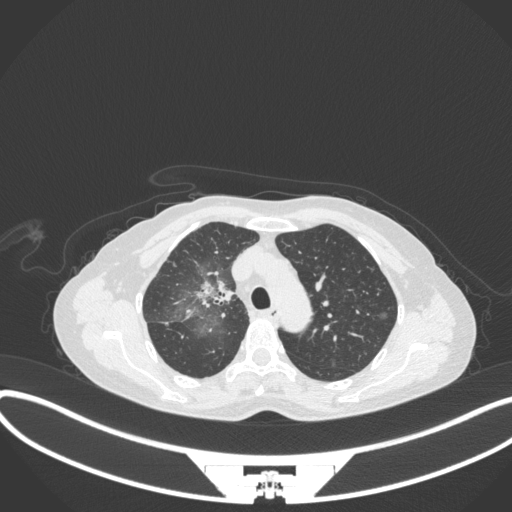
Chest CT, one axial slice. Slice 230 of 311 in the series (ordered by position). Reconstruction kernel B31f. 120 kVp. Lung window (W 1500 / L -600 HU). 512 × 512 image matrix. Patient: female, 59 years. From the clinical record (not read from this slice): clinical TNM (as recorded): T3 N0 M0.
Outlined on this slice (bounding box drawn by a radiologist):
- lung tumour (recorded histology: adenocarcinoma): bounding box [x1, y1, x2, y2] px = [189, 277, 235, 314]